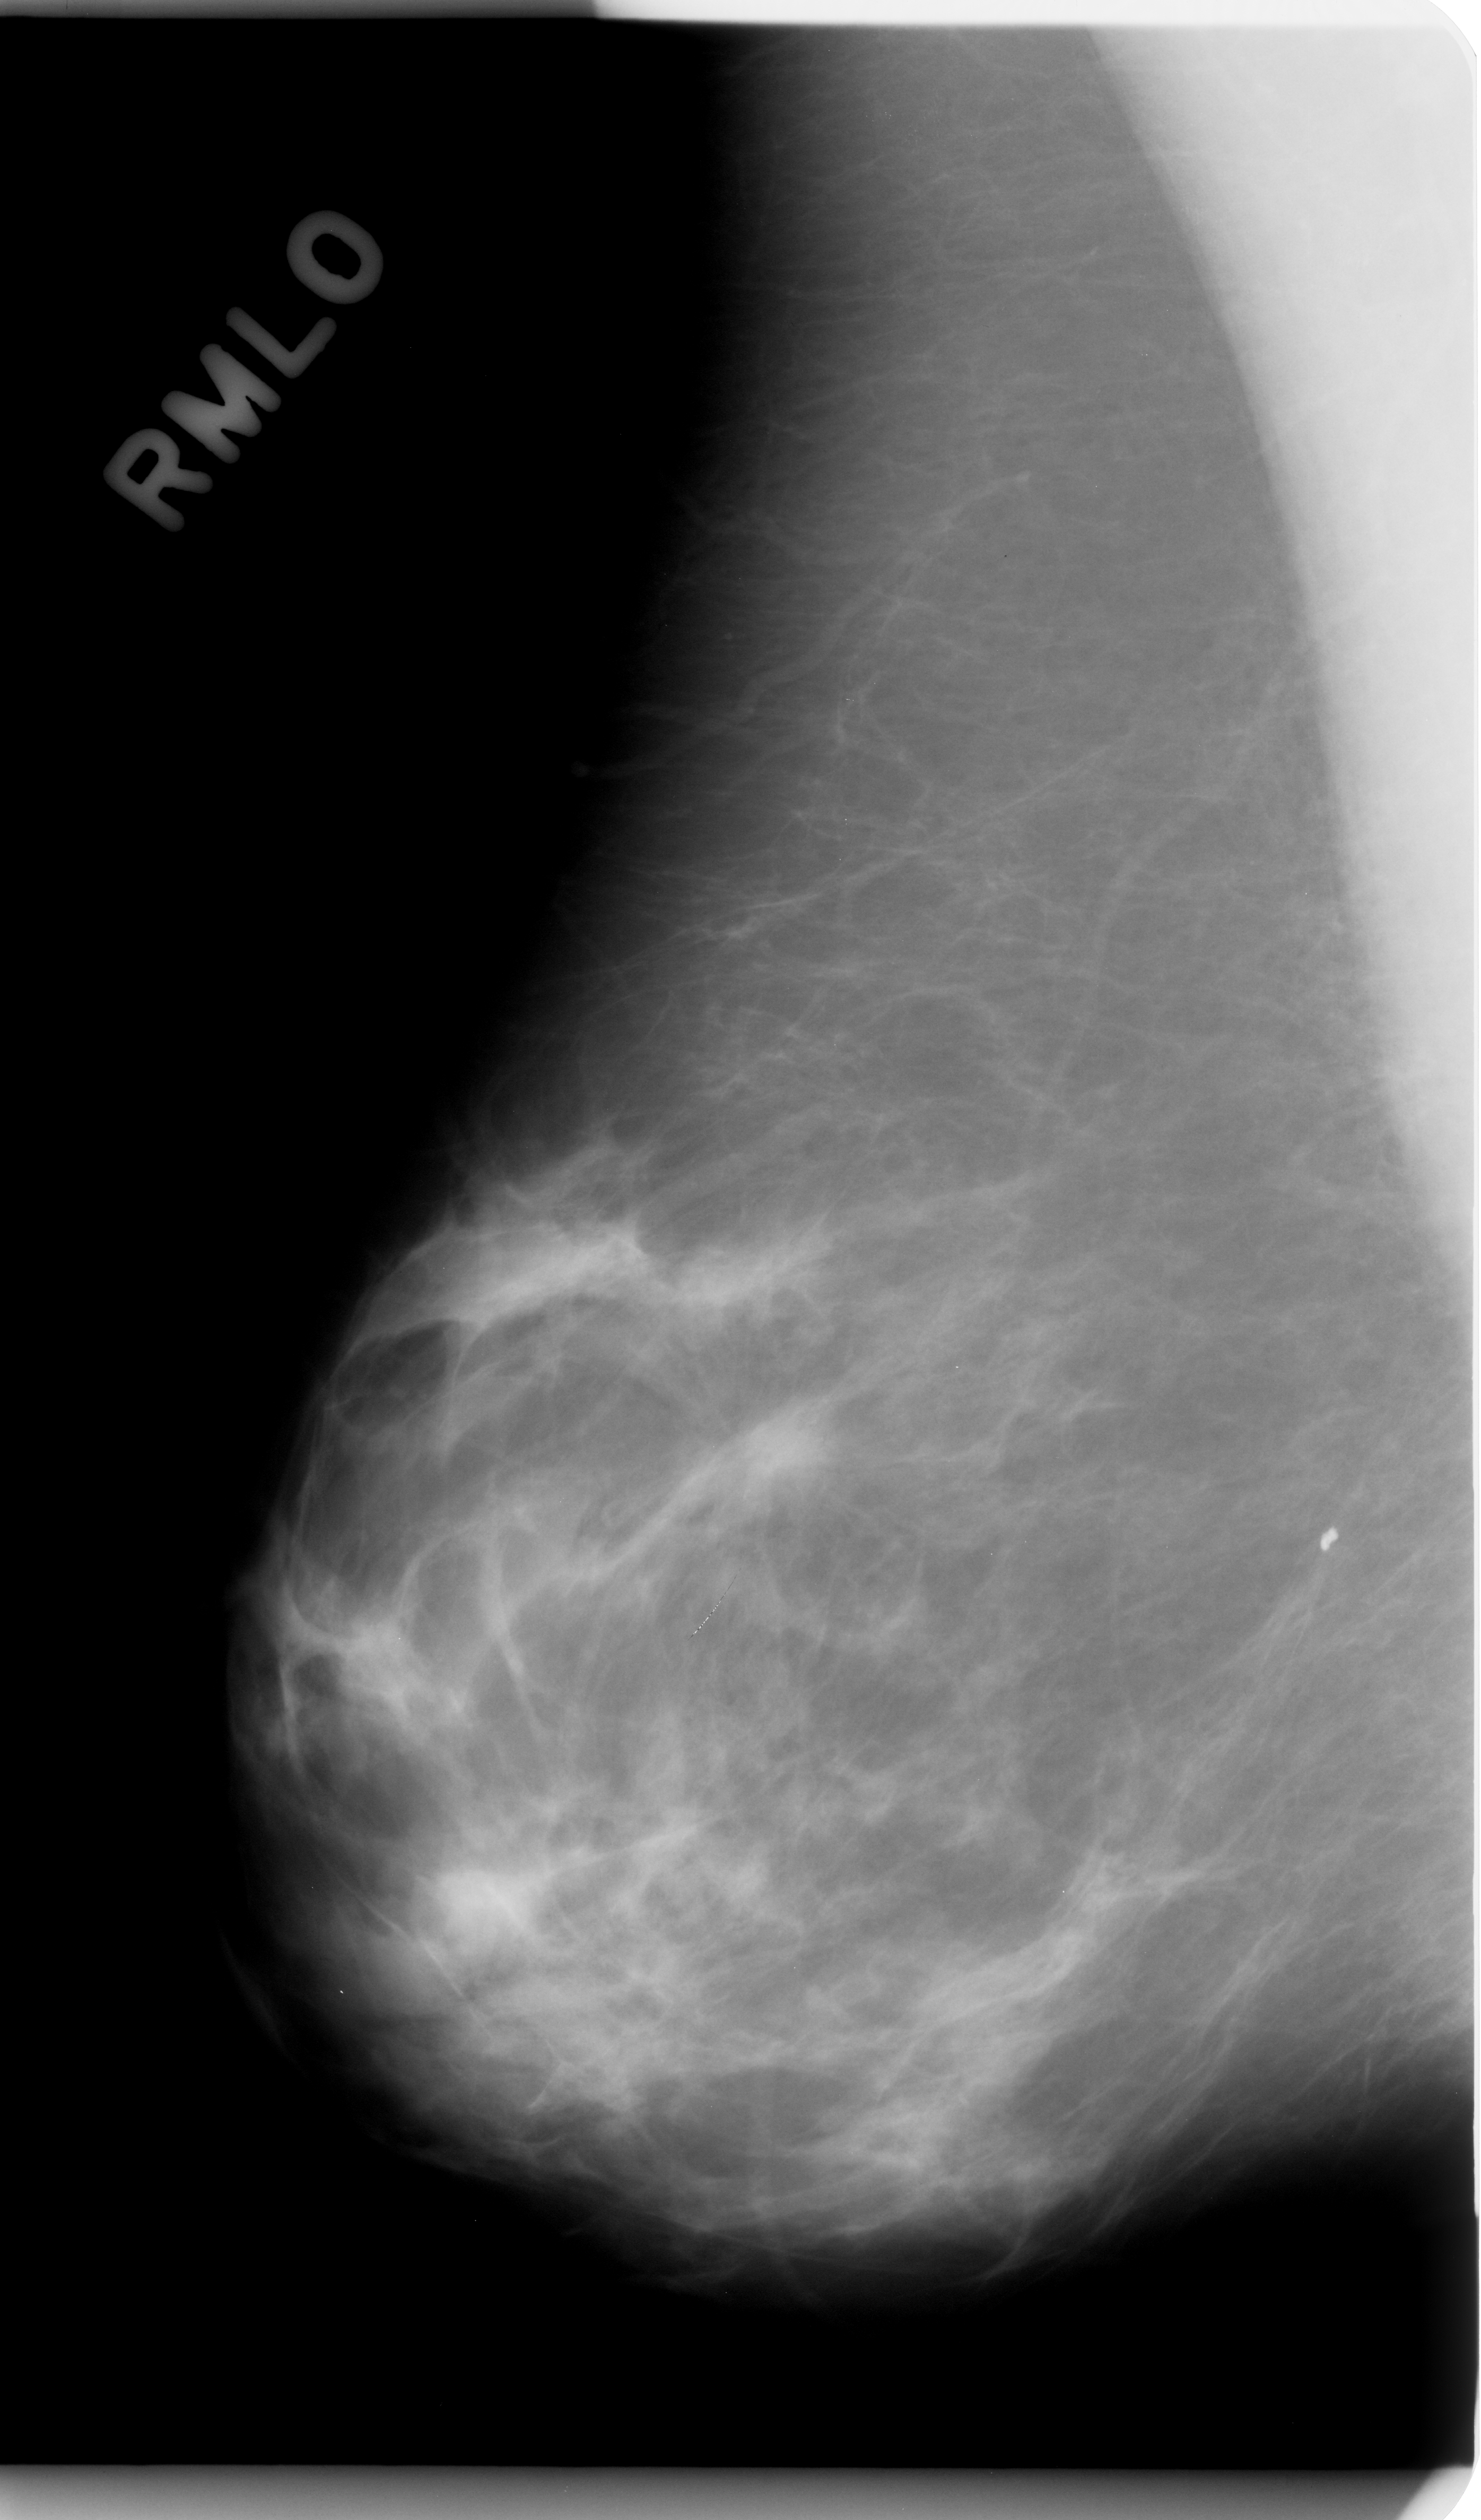
Digitized screen-film mammogram, right breast, mediolateral oblique (MLO) view, BI-RADS breast density category 2 (scale 1–4).
Abnormality record for this image: mass, shape irregular, margins spiculated; BI-RADS assessment category 5; pathology (as recorded): malignant.